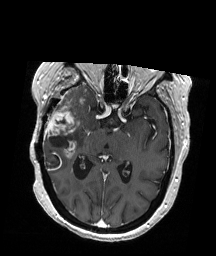
Brain MRI from a brain-tumour surgery series, one axial slice. Slice 110 of 192 in the series (ordered by position). T1-weighted post-contrast. 1 mm slice thickness. 216 × 256 image matrix, field of view 211 × 250 mm. From the clinical record (not read from this slice): histopathology: Glioblastoma; WHO grade: 4; IDH mutation: no.
Annotated regions visible in this slice (outlined manually by an expert reader):
- tumour: box from (x=44, y=86) to (x=89, y=159) px